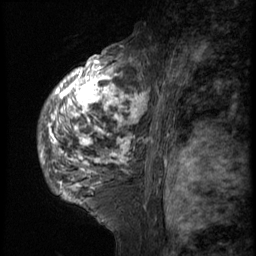
Breast MRI (dynamic contrast-enhanced), one sagittal slice; slice 38 of 58 in the series (ordered by position); 3 images stored at this slice position (order not interpretable as contrast timing); 1.5 T; TE 4.2 ms, TR 9 ms; 2.5 mm slice thickness; 256 × 256 image matrix, field of view 180 × 180 mm. Female patient, age 50 years. From the clinical record (not read from this slice): setting: breast cancer imaged before/during neoadjuvant chemotherapy; receptor status: triple-negative.
Structures marked on this image (semi-automatically segmented with operator editing):
- analysis volume of interest (the breast-tissue region the enhancement analysis was run in; not a lesion): box from (x=38, y=48) to (x=135, y=214) px
- tumour enhancement mask (voxels above the 140 % enhancement threshold inside the analysis volume of interest): (x=39, y=55)–(x=135, y=203)